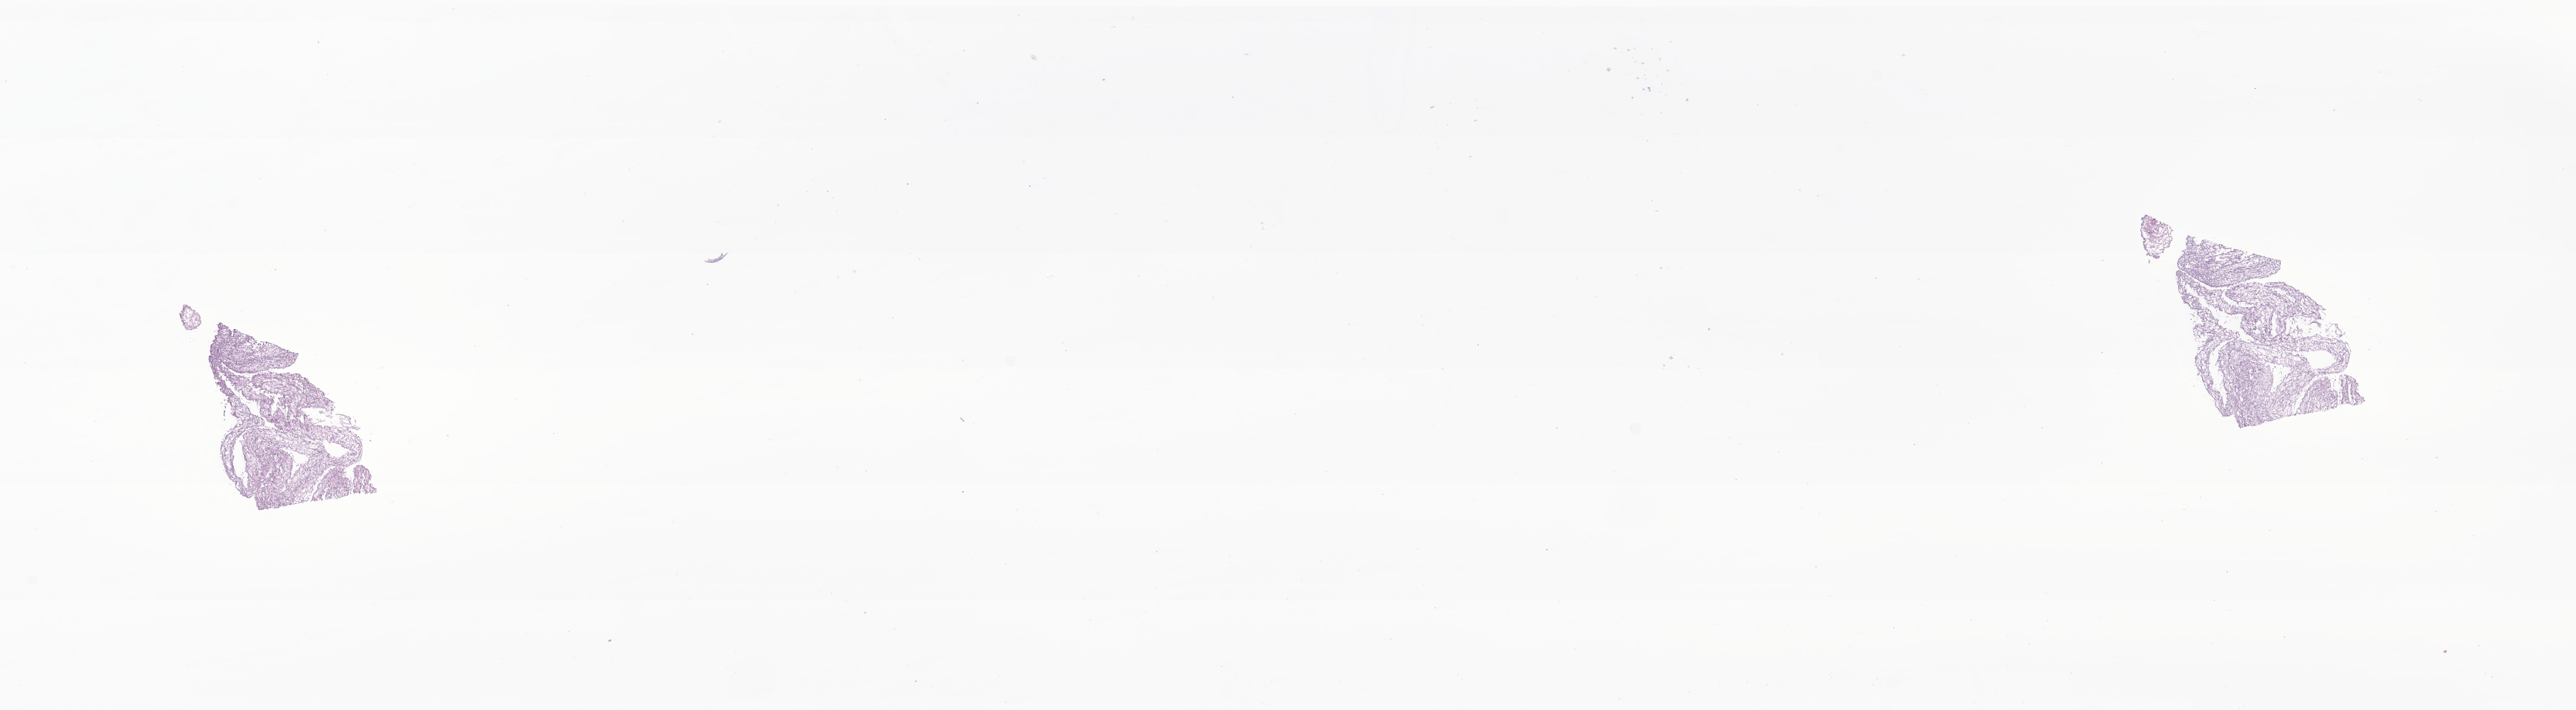
Digitized hematoxylin and eosin (H&E)-stained section of tumor tissue from the lung, shown as a low-resolution overview of the whole scanned area (about 23.8 x 6.6 mm); frozen section (OCT-embedded). Patient female; age 371 days.
Diagnosis (ICD-O-3 morphology term): Pleuropulmonary blastoma.